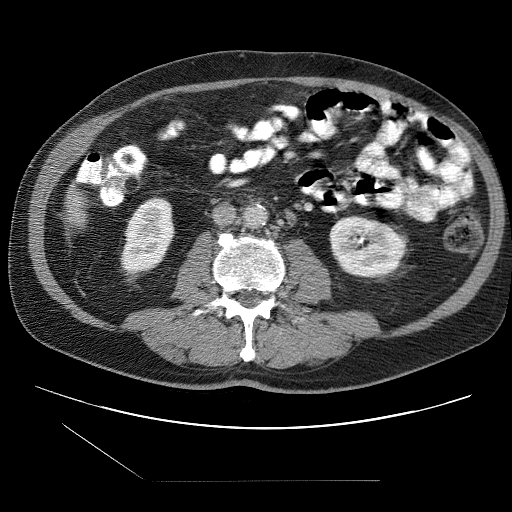
Contrast-enhanced abdominal CT (liver protocol), one axial slice. Slice 8 of 109 in the series (ordered by position). Reconstruction kernel STANDARD. 120 kVp. One of 2 acquisitions stored at this slice position. Soft-tissue window (W 400 / L 40 HU). 2.5 mm slice thickness. 512 × 512 image matrix, field of view 400 × 400 mm. From the clinical record (not read from this slice): diagnosis: hepatocellular carcinoma (patient treated with transarterial chemoembolisation; whether this scan precedes or follows treatment is not stated here); TNM stage (as recorded): Stage-IIIB; Child-Pugh class: A; tumour differentiation: well differentiated; tumour nodularity: multinodular.
Annotated regions visible in this slice (semi-automatic segmentation, software-assisted and operator-edited):
- liver parenchyma outside the tumour (the mass and vessels are separate outlines, so this box may not span the whole liver): bounding box <66,188,85,225> (left, top, right, bottom; pixels)